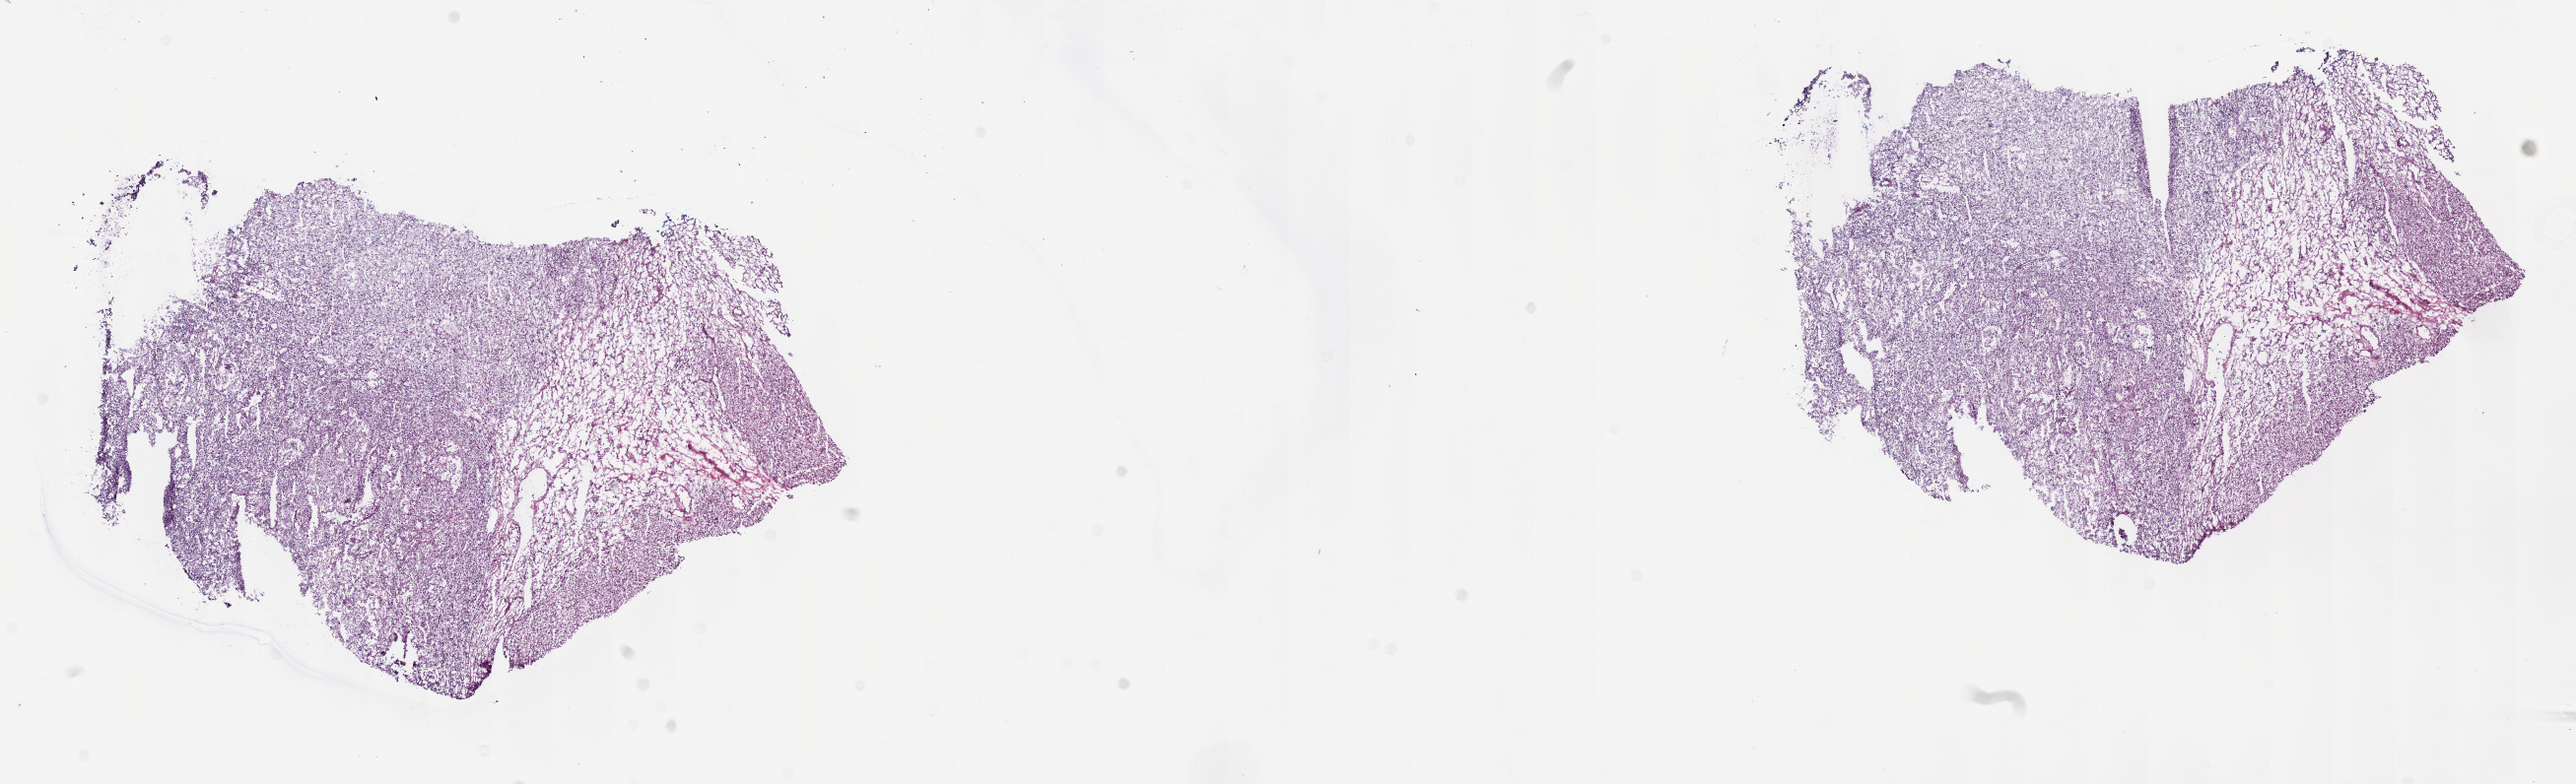
Whole-slide histology image, H&E-stained, low-resolution overview of the scanned area, about 21.1 x 6.4 mm (from a 40x scan), frozen section, sample: primary tumour, kidney. Patient: female, age at initial diagnosis 74 years. Histologic grade: G1 (well differentiated). Slide review estimates, as recorded: tumour cells 83%, tumour nuclei 95%, normal cells 0%, stromal cells 16%, necrosis 1%. Infiltration values recorded for this section: lymphocyte infiltration 2%, monocyte infiltration 2%, neutrophil infiltration 0%.
* AJCC pathologic stage: I (7th edition)
* diagnosis: Clear cell adenocarcinoma, NOS
* laterality: right